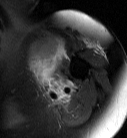
MRI of an extremity soft-tissue mass, one axial slice; position 59 of 87 along the scan axis; T2-weighted fat-saturated; MR volume resampled by the dataset authors to the PET/CT grid (not the native acquisition matrix); 3.27 mm slice thickness; 127 × 138 image matrix. Female patient. From the clinical record (not read from this slice): histological type: pleiomorphic leiomyosarcoma; grade: high; site of the primary tumour: left biceps.
Annotated regions visible in this slice (expert contour drawn on MRI and transferred to this co-registered scan by the dataset authors):
- gross tumour volume including surrounding oedema: bounding box <29,36,66,90> (left, top, right, bottom; pixels)
- gross tumour volume (mass): <27,39,62,78>